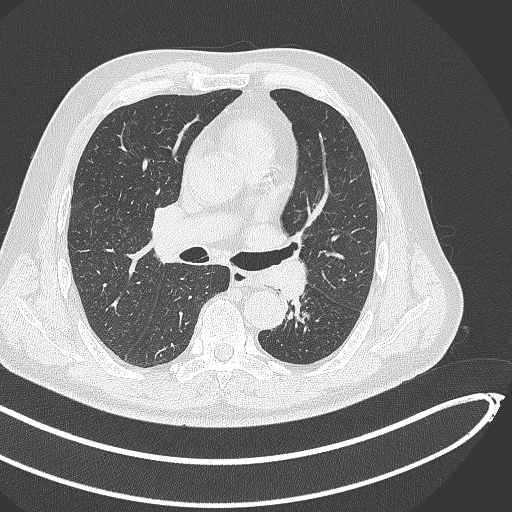
Chest CT, one axial slice; position 270 of 468 along the scan axis; reconstruction kernel B70f; lung window (W 1500 / L -600 HU); 1 mm slice thickness; 512 × 512 image matrix. Patient: male, 64 years. From the clinical record (not read from this slice): clinical TNM (as recorded): T1c N0 M0.
Annotated regions visible in this slice (bounding box drawn by a radiologist):
- lung tumour (recorded histology: squamous cell carcinoma): bounding box <262,255,309,301> (left, top, right, bottom; pixels)